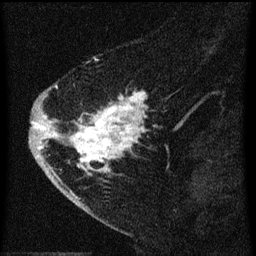
Breast MRI (dynamic contrast-enhanced), one sagittal slice; position 19 of 60 along the scan axis; dynamic contrast-enhanced series, image 2 of 3 at this slice position (ordered by acquisition); 1.5 T; TE 4.2 ms, TR 8 ms; 256 × 256 image matrix, field of view 180 × 180 mm. Female patient, age 47 years.
Structures marked on this image (semi-automatic segmentation, software-assisted and operator-edited):
- analysis volume of interest (the breast-tissue region the enhancement analysis was run in; not a lesion): bounding box <38,76,158,193> (left, top, right, bottom; pixels)
- tumour enhancement mask (voxels above the 70 % enhancement threshold inside the analysis volume of interest): <38,84,155,193>